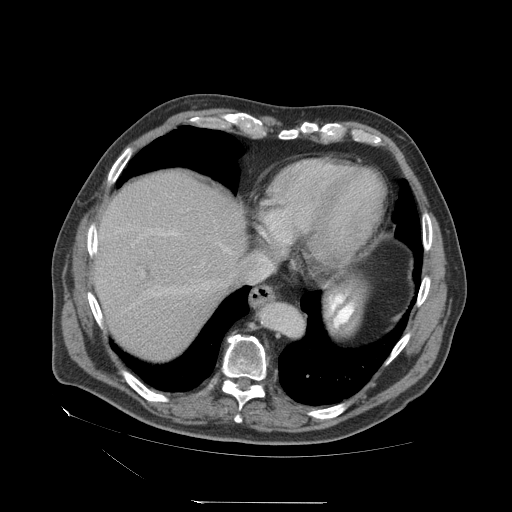
Contrast-enhanced abdominal CT (liver protocol), one axial slice; slice 61 of 83 in the series (ordered by position); reconstruction kernel STANDARD; soft-tissue window (W 400 / L 40 HU); 2.5 mm slice thickness; 512 × 512 image matrix, field of view 460 × 460 mm. Case-level facts recorded for this patient, not image findings: diagnosis: hepatocellular carcinoma (patient treated with transarterial chemoembolisation; whether this scan precedes or follows treatment is not stated here); TNM stage (as recorded): Stage-I; Child-Pugh class: A; tumour differentiation: well differentiated; tumour nodularity: uninodular.
Structures marked on this image (semi-automatically segmented with operator editing):
- abdominal aorta: box from (x=262, y=303) to (x=303, y=336) px
- liver parenchyma outside the tumour (the mass and vessels are separate outlines, so this box may not span the whole liver): (x=94, y=170)–(x=246, y=360)
- liver vessels: (x=116, y=231)–(x=178, y=295)